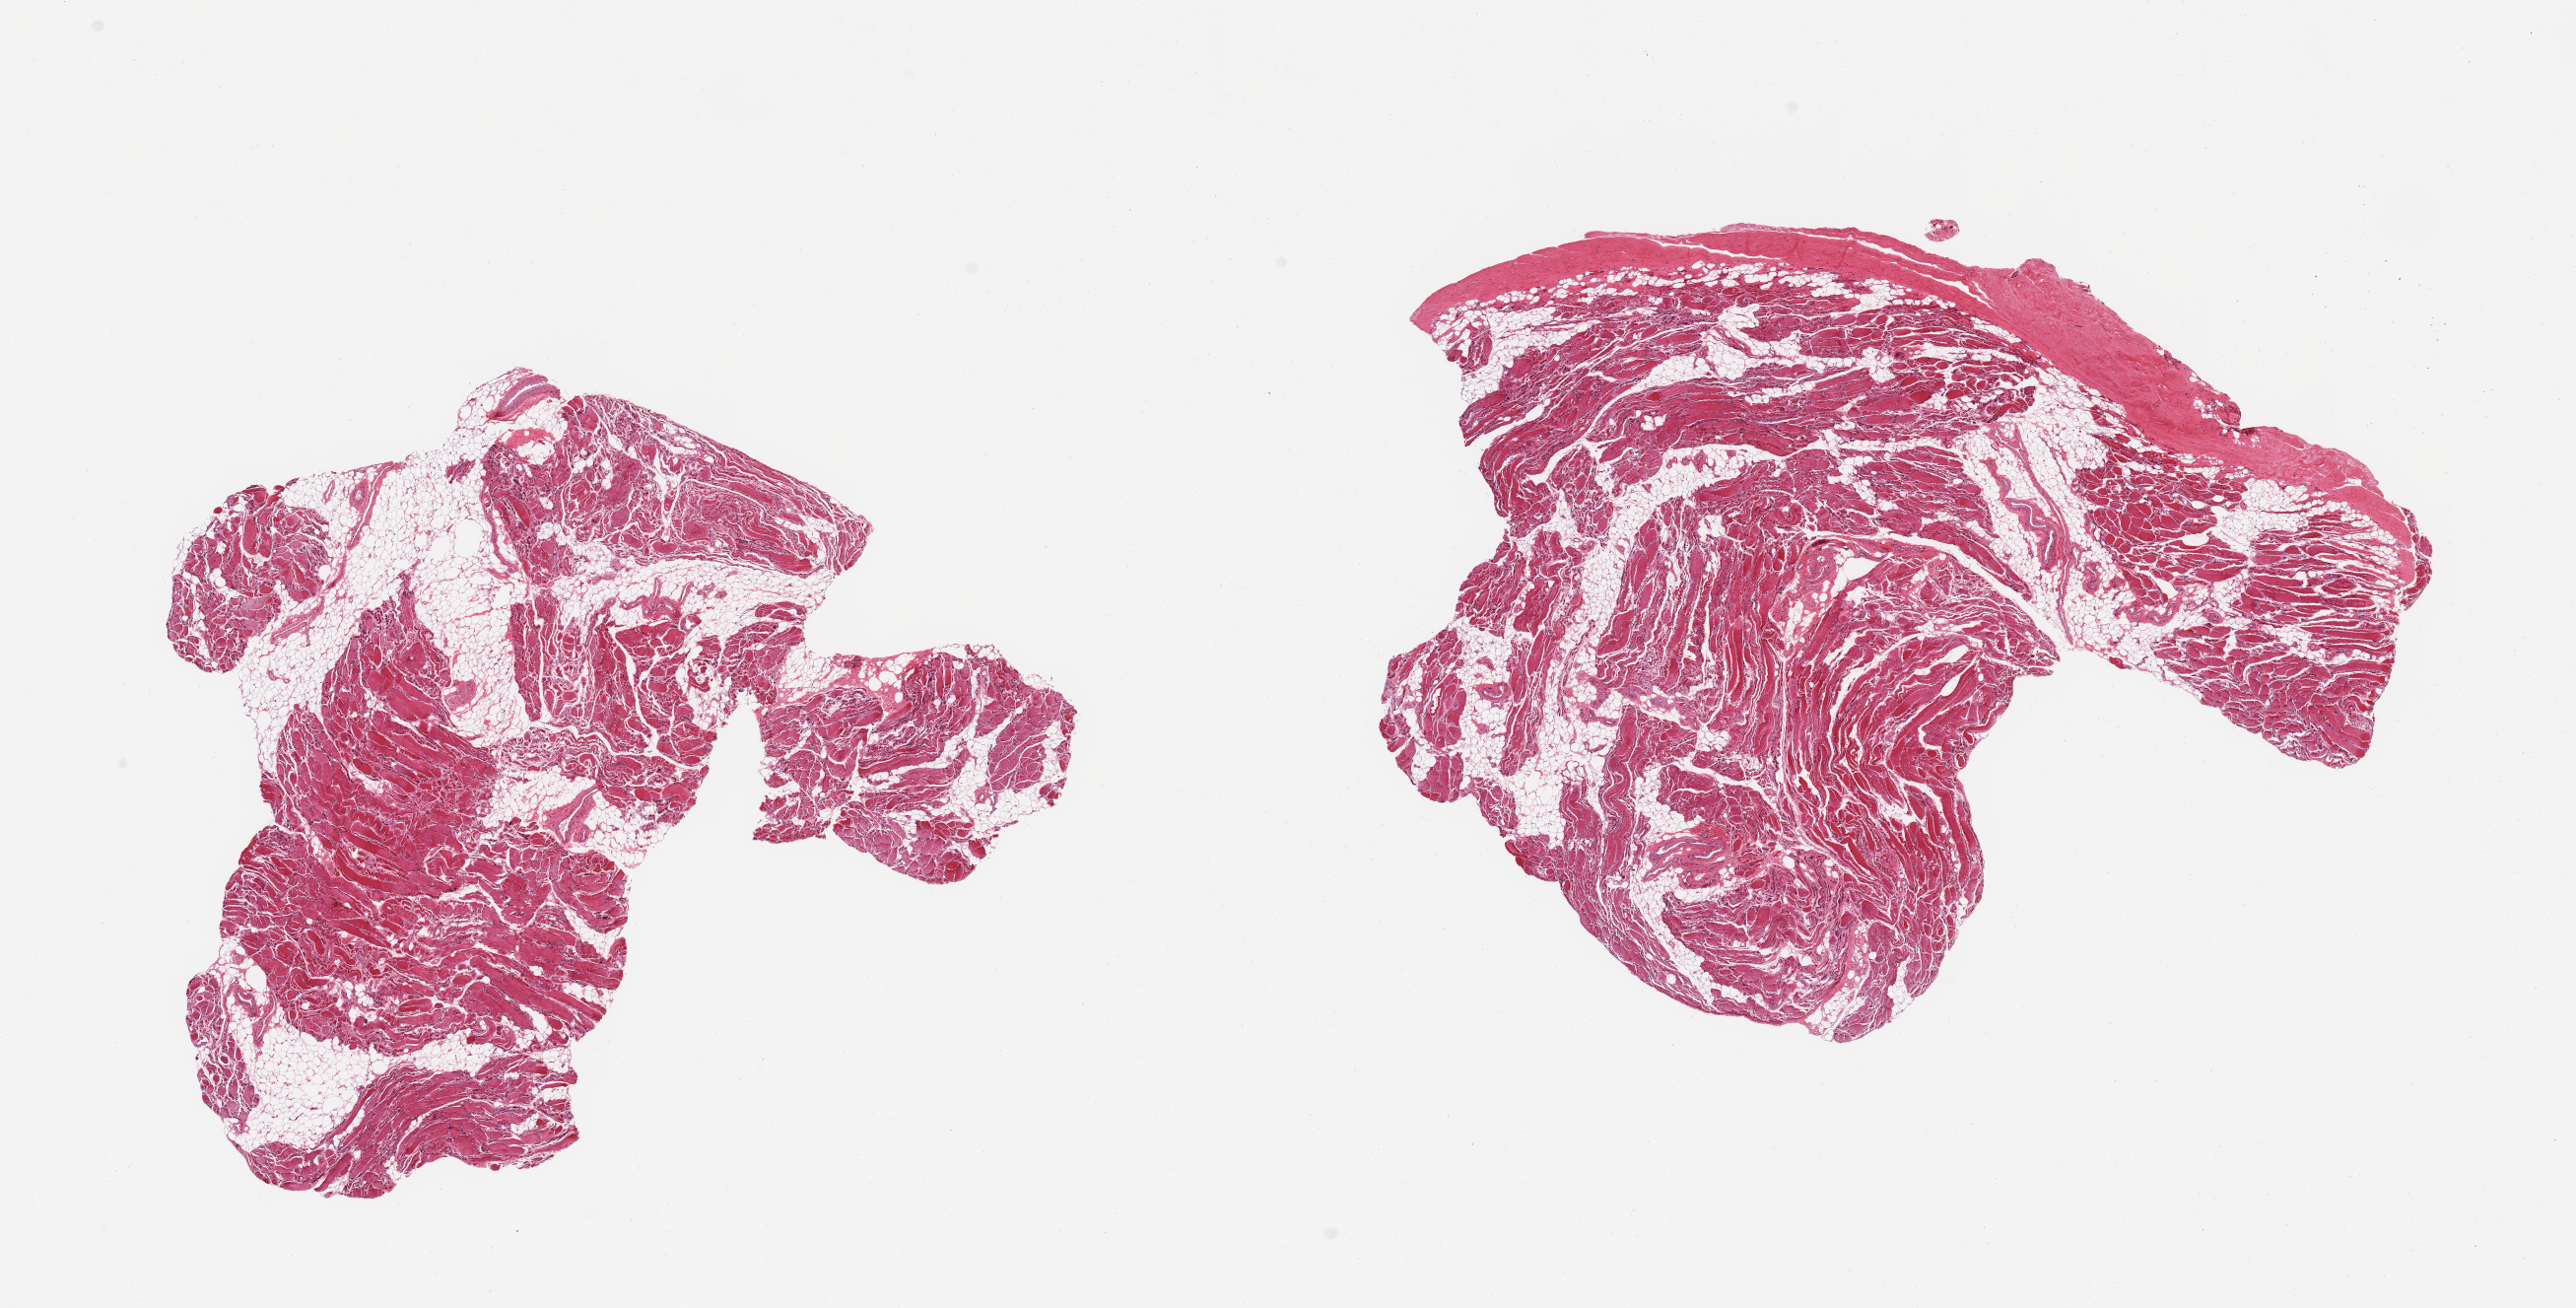
Digitized hematoxylin and eosin (H&E)-stained section, shown as a low-resolution overview of the whole scanned area (about 20.7 x 10.5 mm, slide scanned at 20x). PAXgene-fixed paraffin-embedded (PFPE) section. Target tissue: skeletal muscle. Donor tissue sample. Donor sex: female.
* review note (as recorded): 2 pieces; atrophy & 20% internal fat